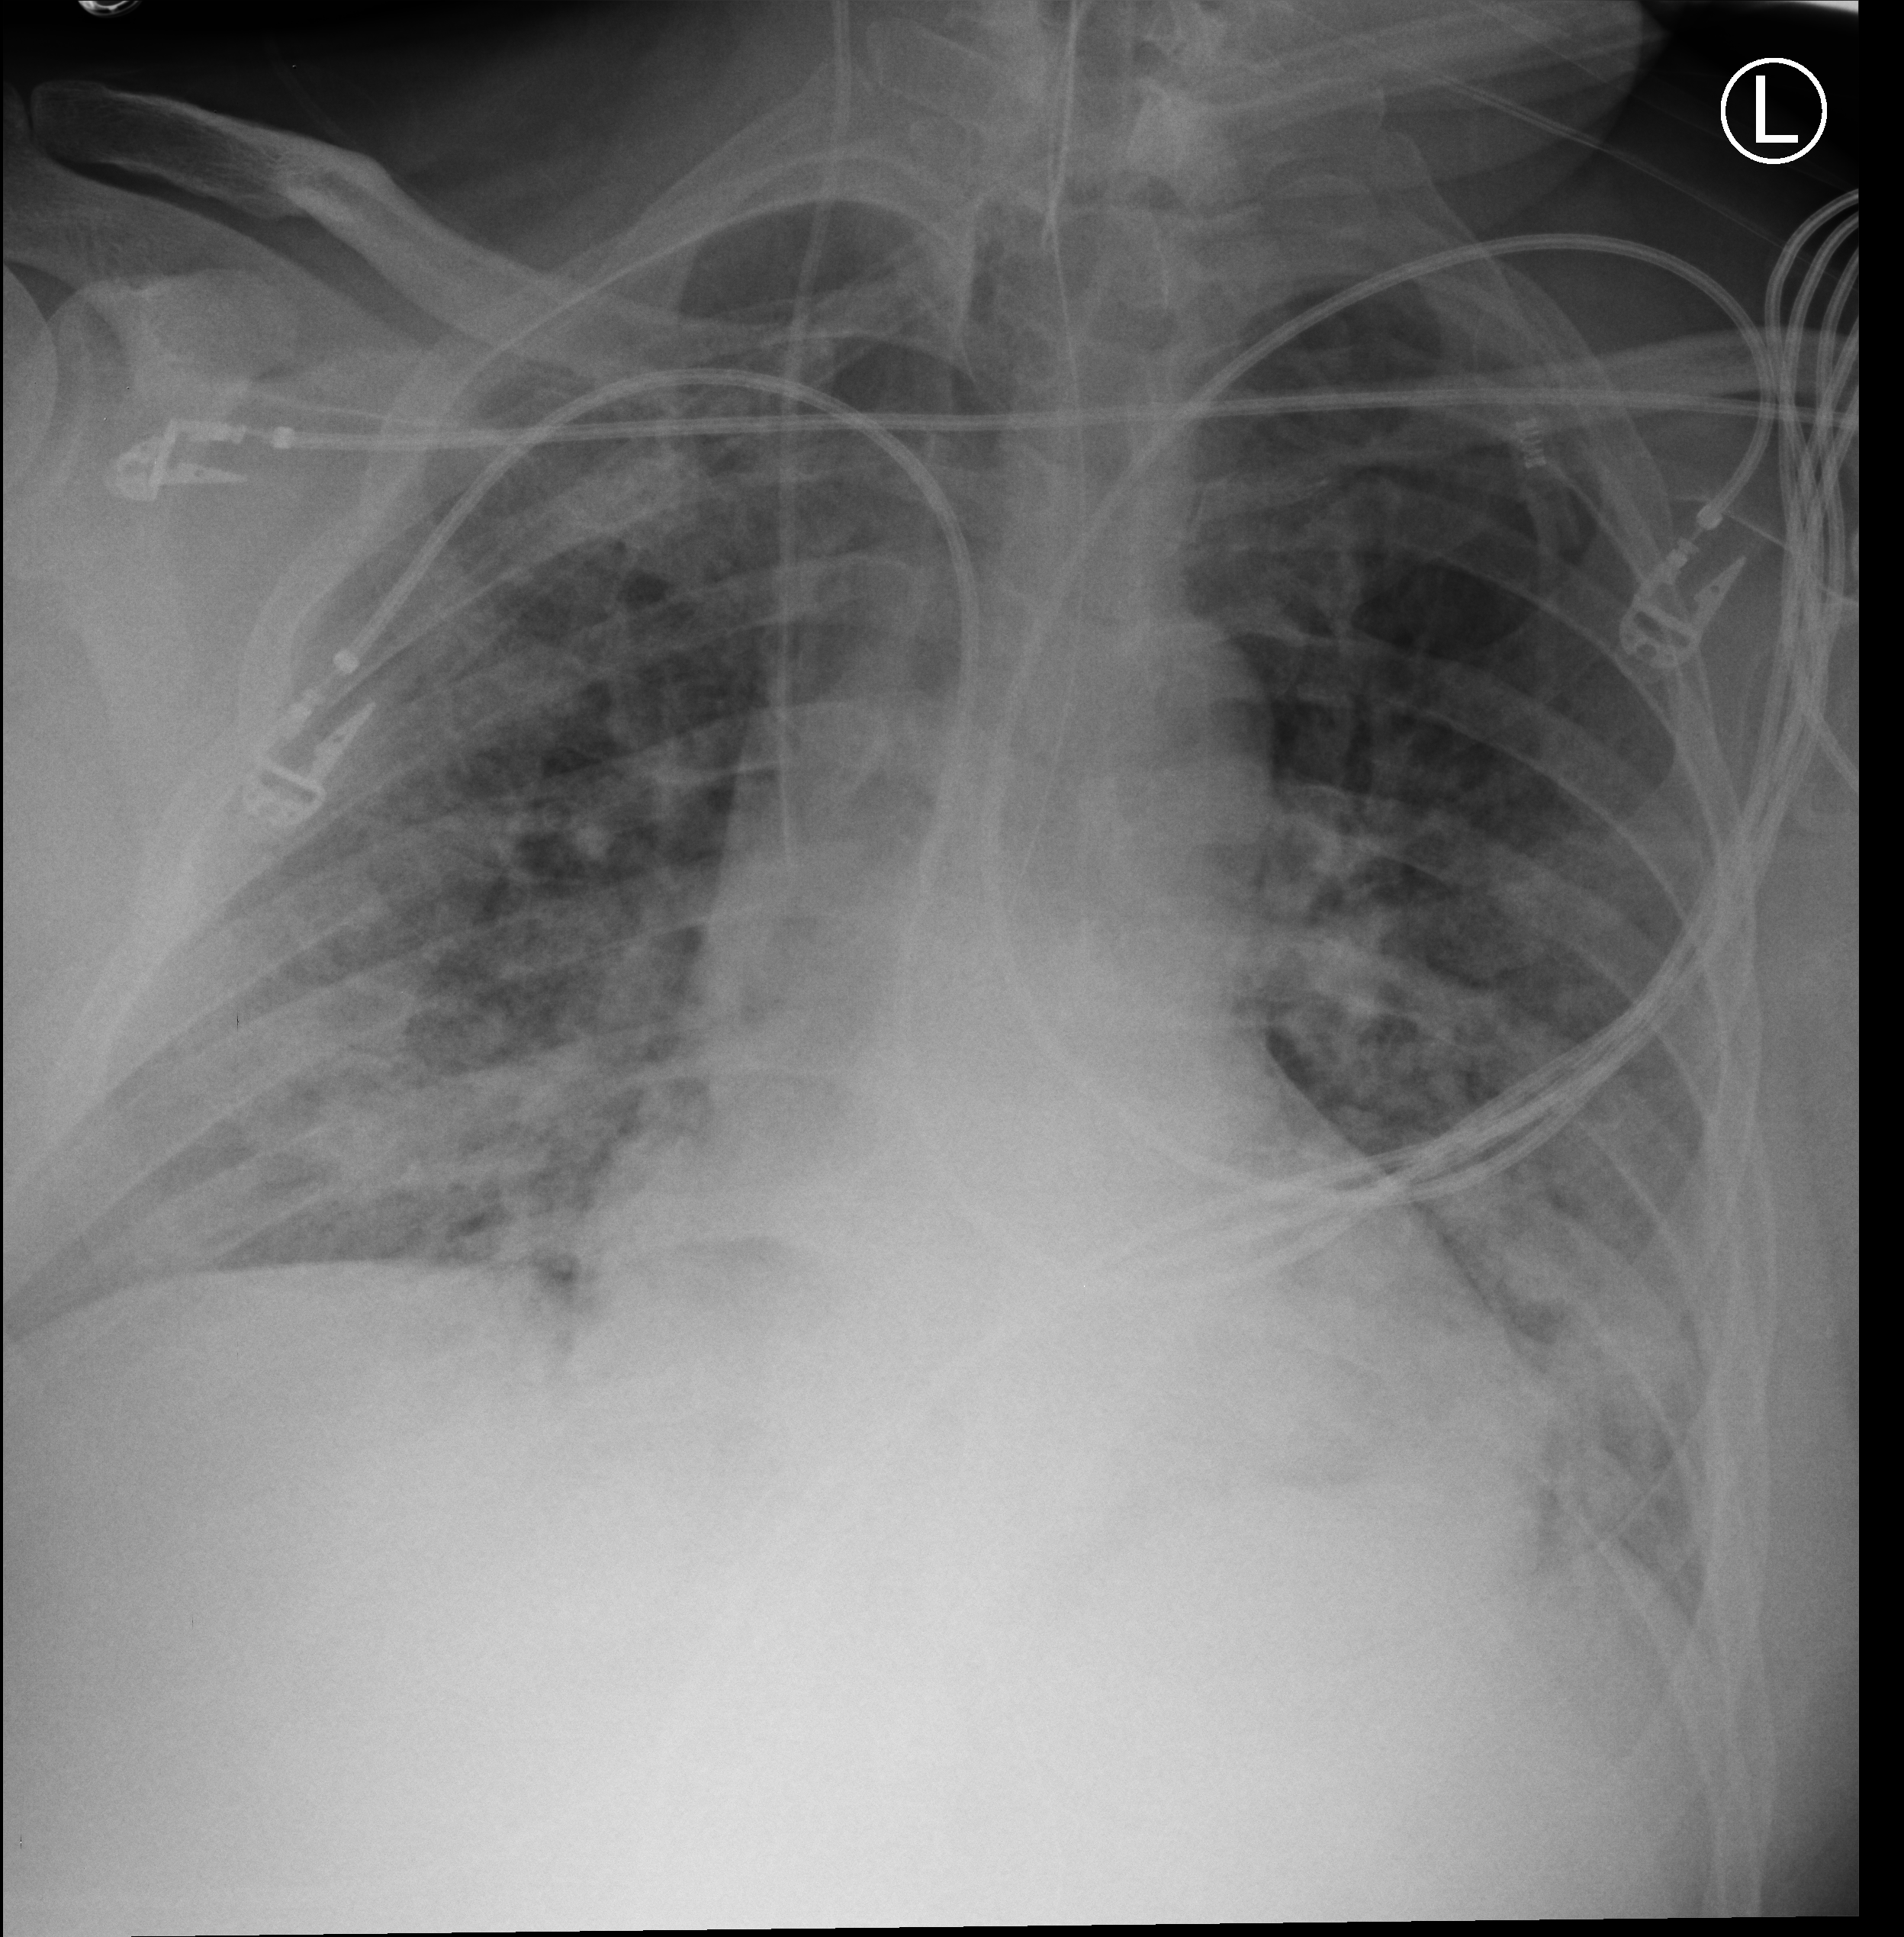
Portable chest radiograph, anteroposterior (AP) projection. Patient hospitalised with COVID-19; male, aged 18–59 years.
Admission-level facts for this patient (not findings on this image; timing relative to this image not recorded): admitted to intensive care during this hospital stay: no.